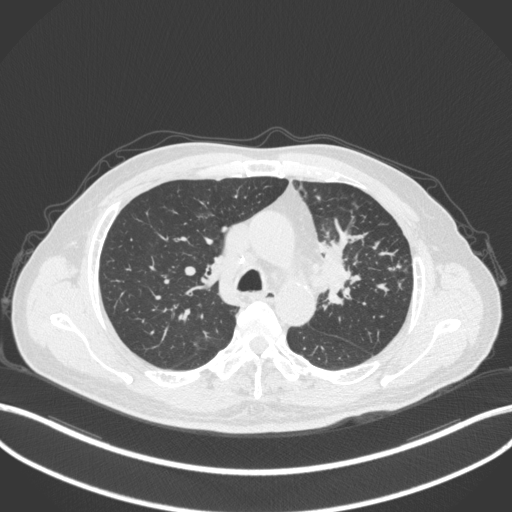
Chest CT, one axial slice. Slice 237 of 386 in the series (ordered by position). 120 kVp. Lung window (W 1500 / L -600 HU). 1 mm slice thickness. 512 × 512 image matrix, field of view 400 × 400 mm. Male patient, age 69 years. From the clinical record (not read from this slice): clinical TNM (as recorded): T2a N2 M0; histopathological grade: G2-3.
Structures marked on this image (rectangle marked by the reading radiologist):
- lung tumour (recorded histology: adenocarcinoma): box from (x=321, y=228) to (x=356, y=309) px